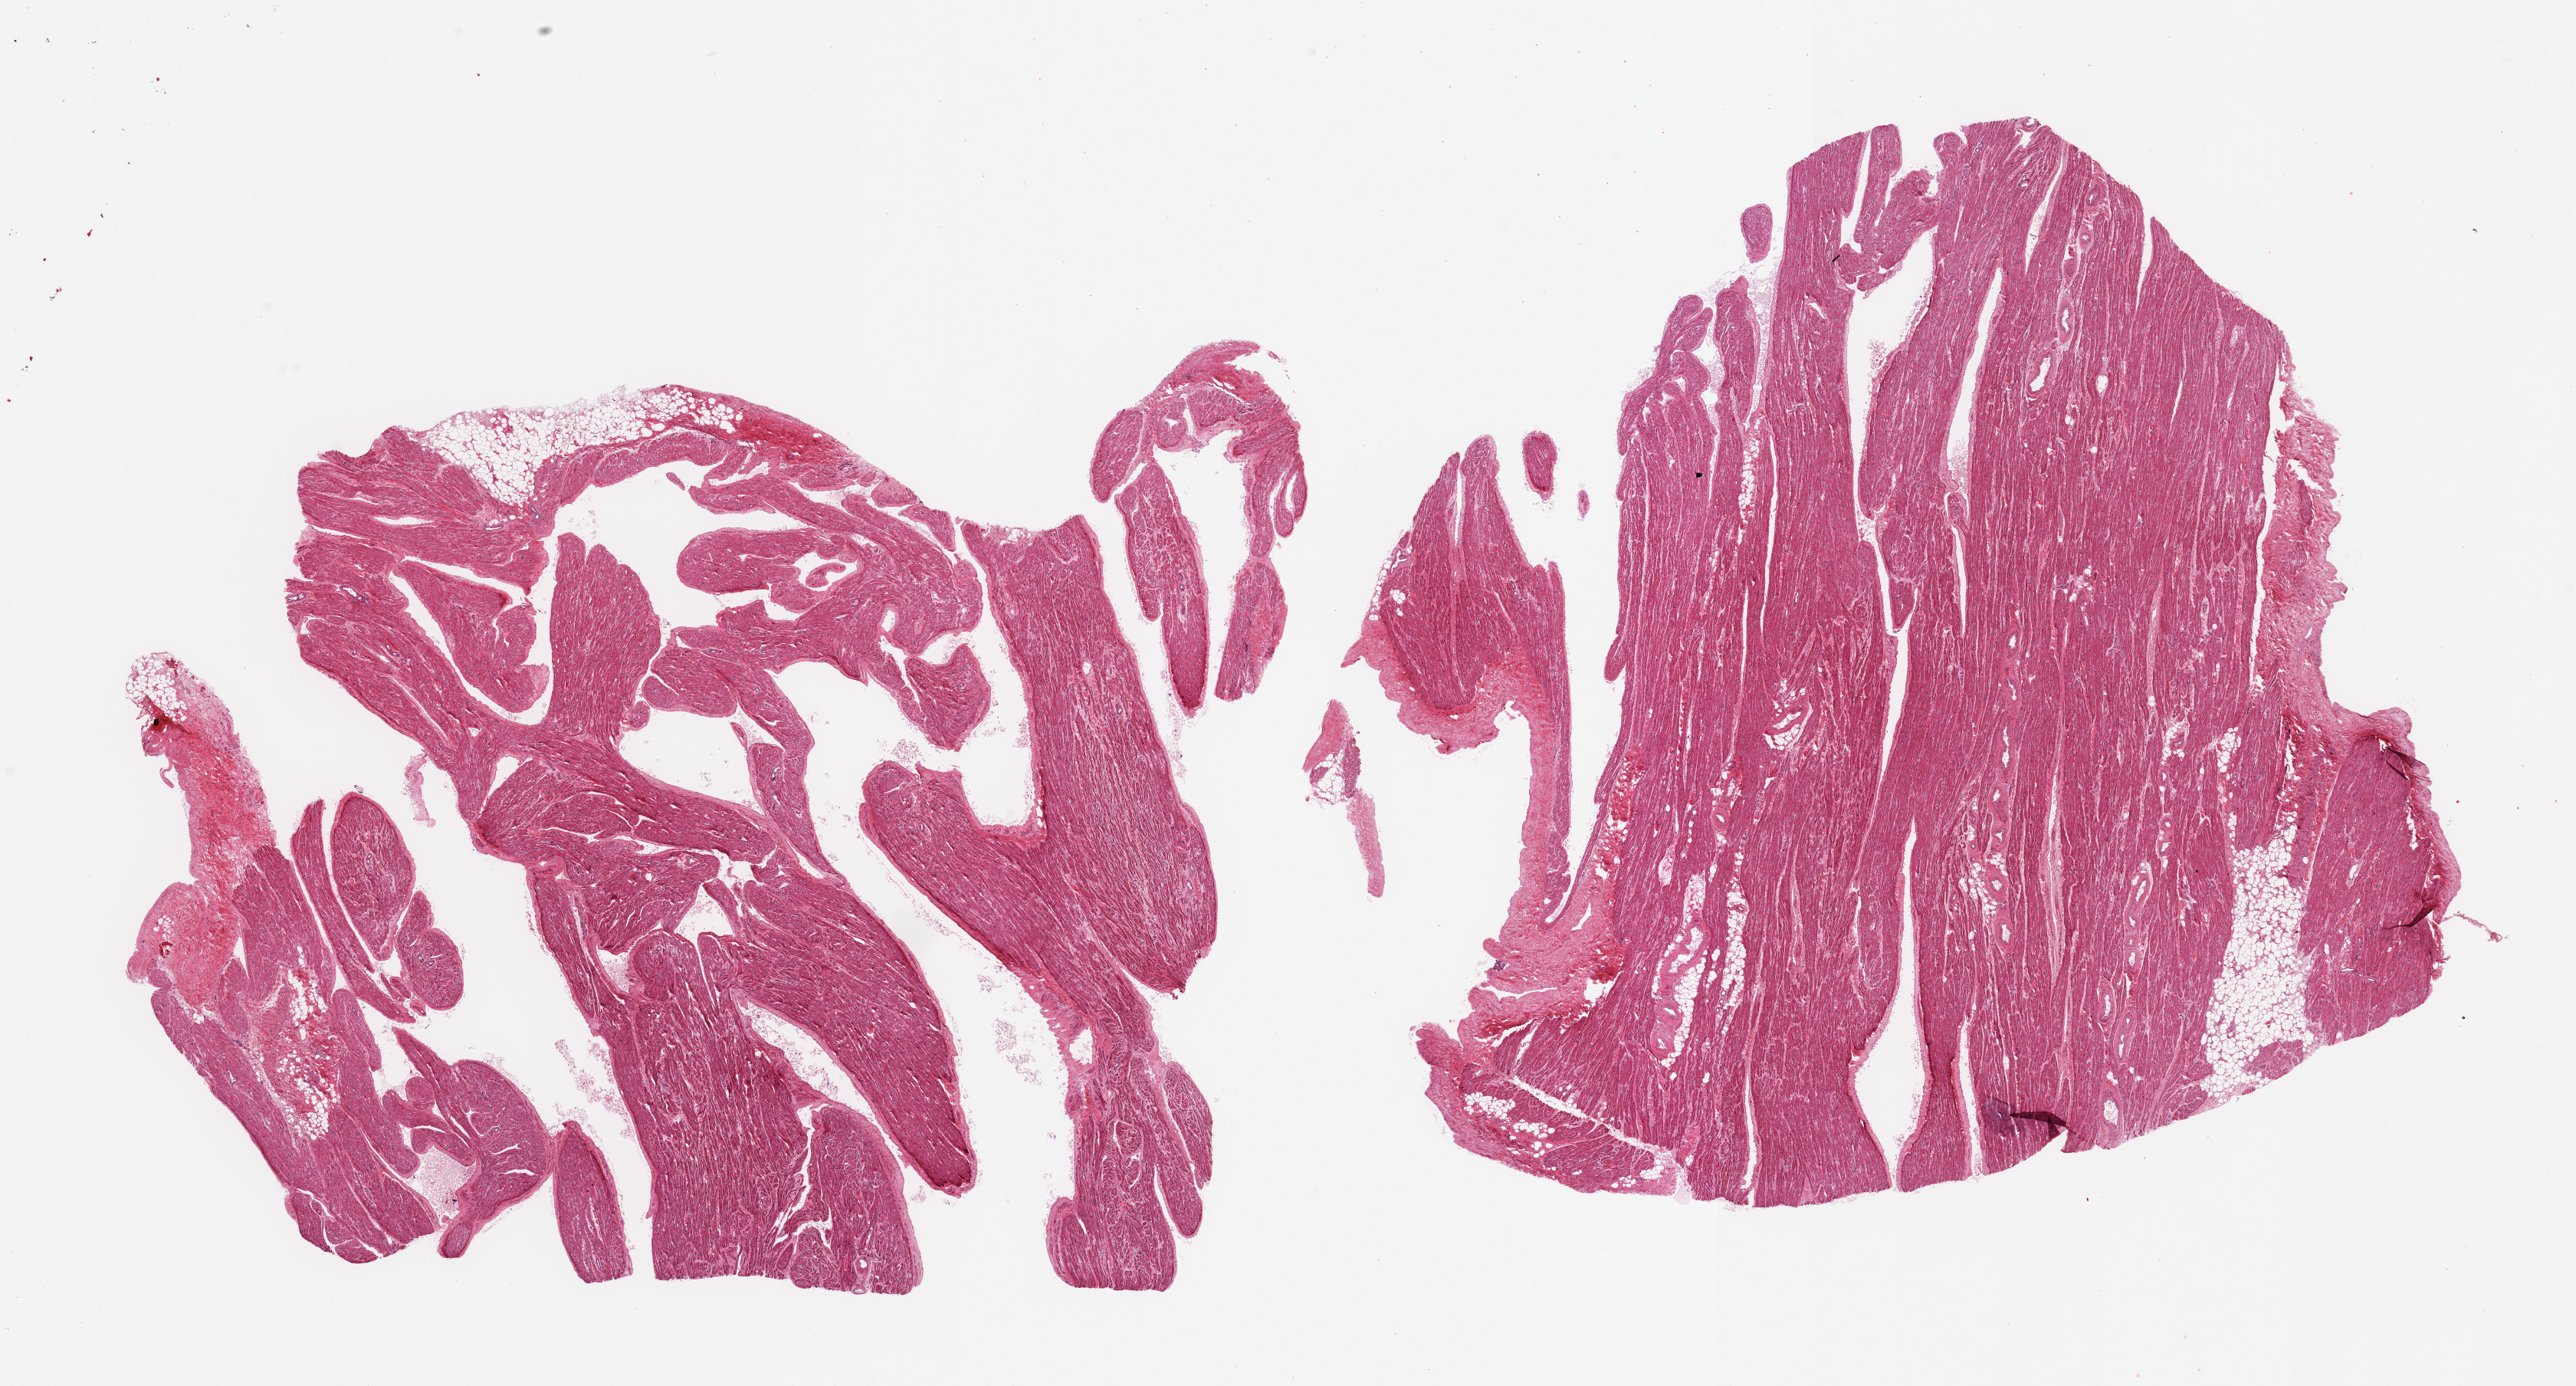
Whole-slide image, haematoxylin and eosin stain — whole scanned area (about 26.6 x 14.3 mm, acquisition: 20x scan) shown as a low-resolution overview; PAXgene-fixed, paraffin-embedded tissue; section of auricular appendage (target tissue); tissue donor sample. Donor sex: male.
• reviewer comment on this tissue sample: 2 pieces; 5% internal fat